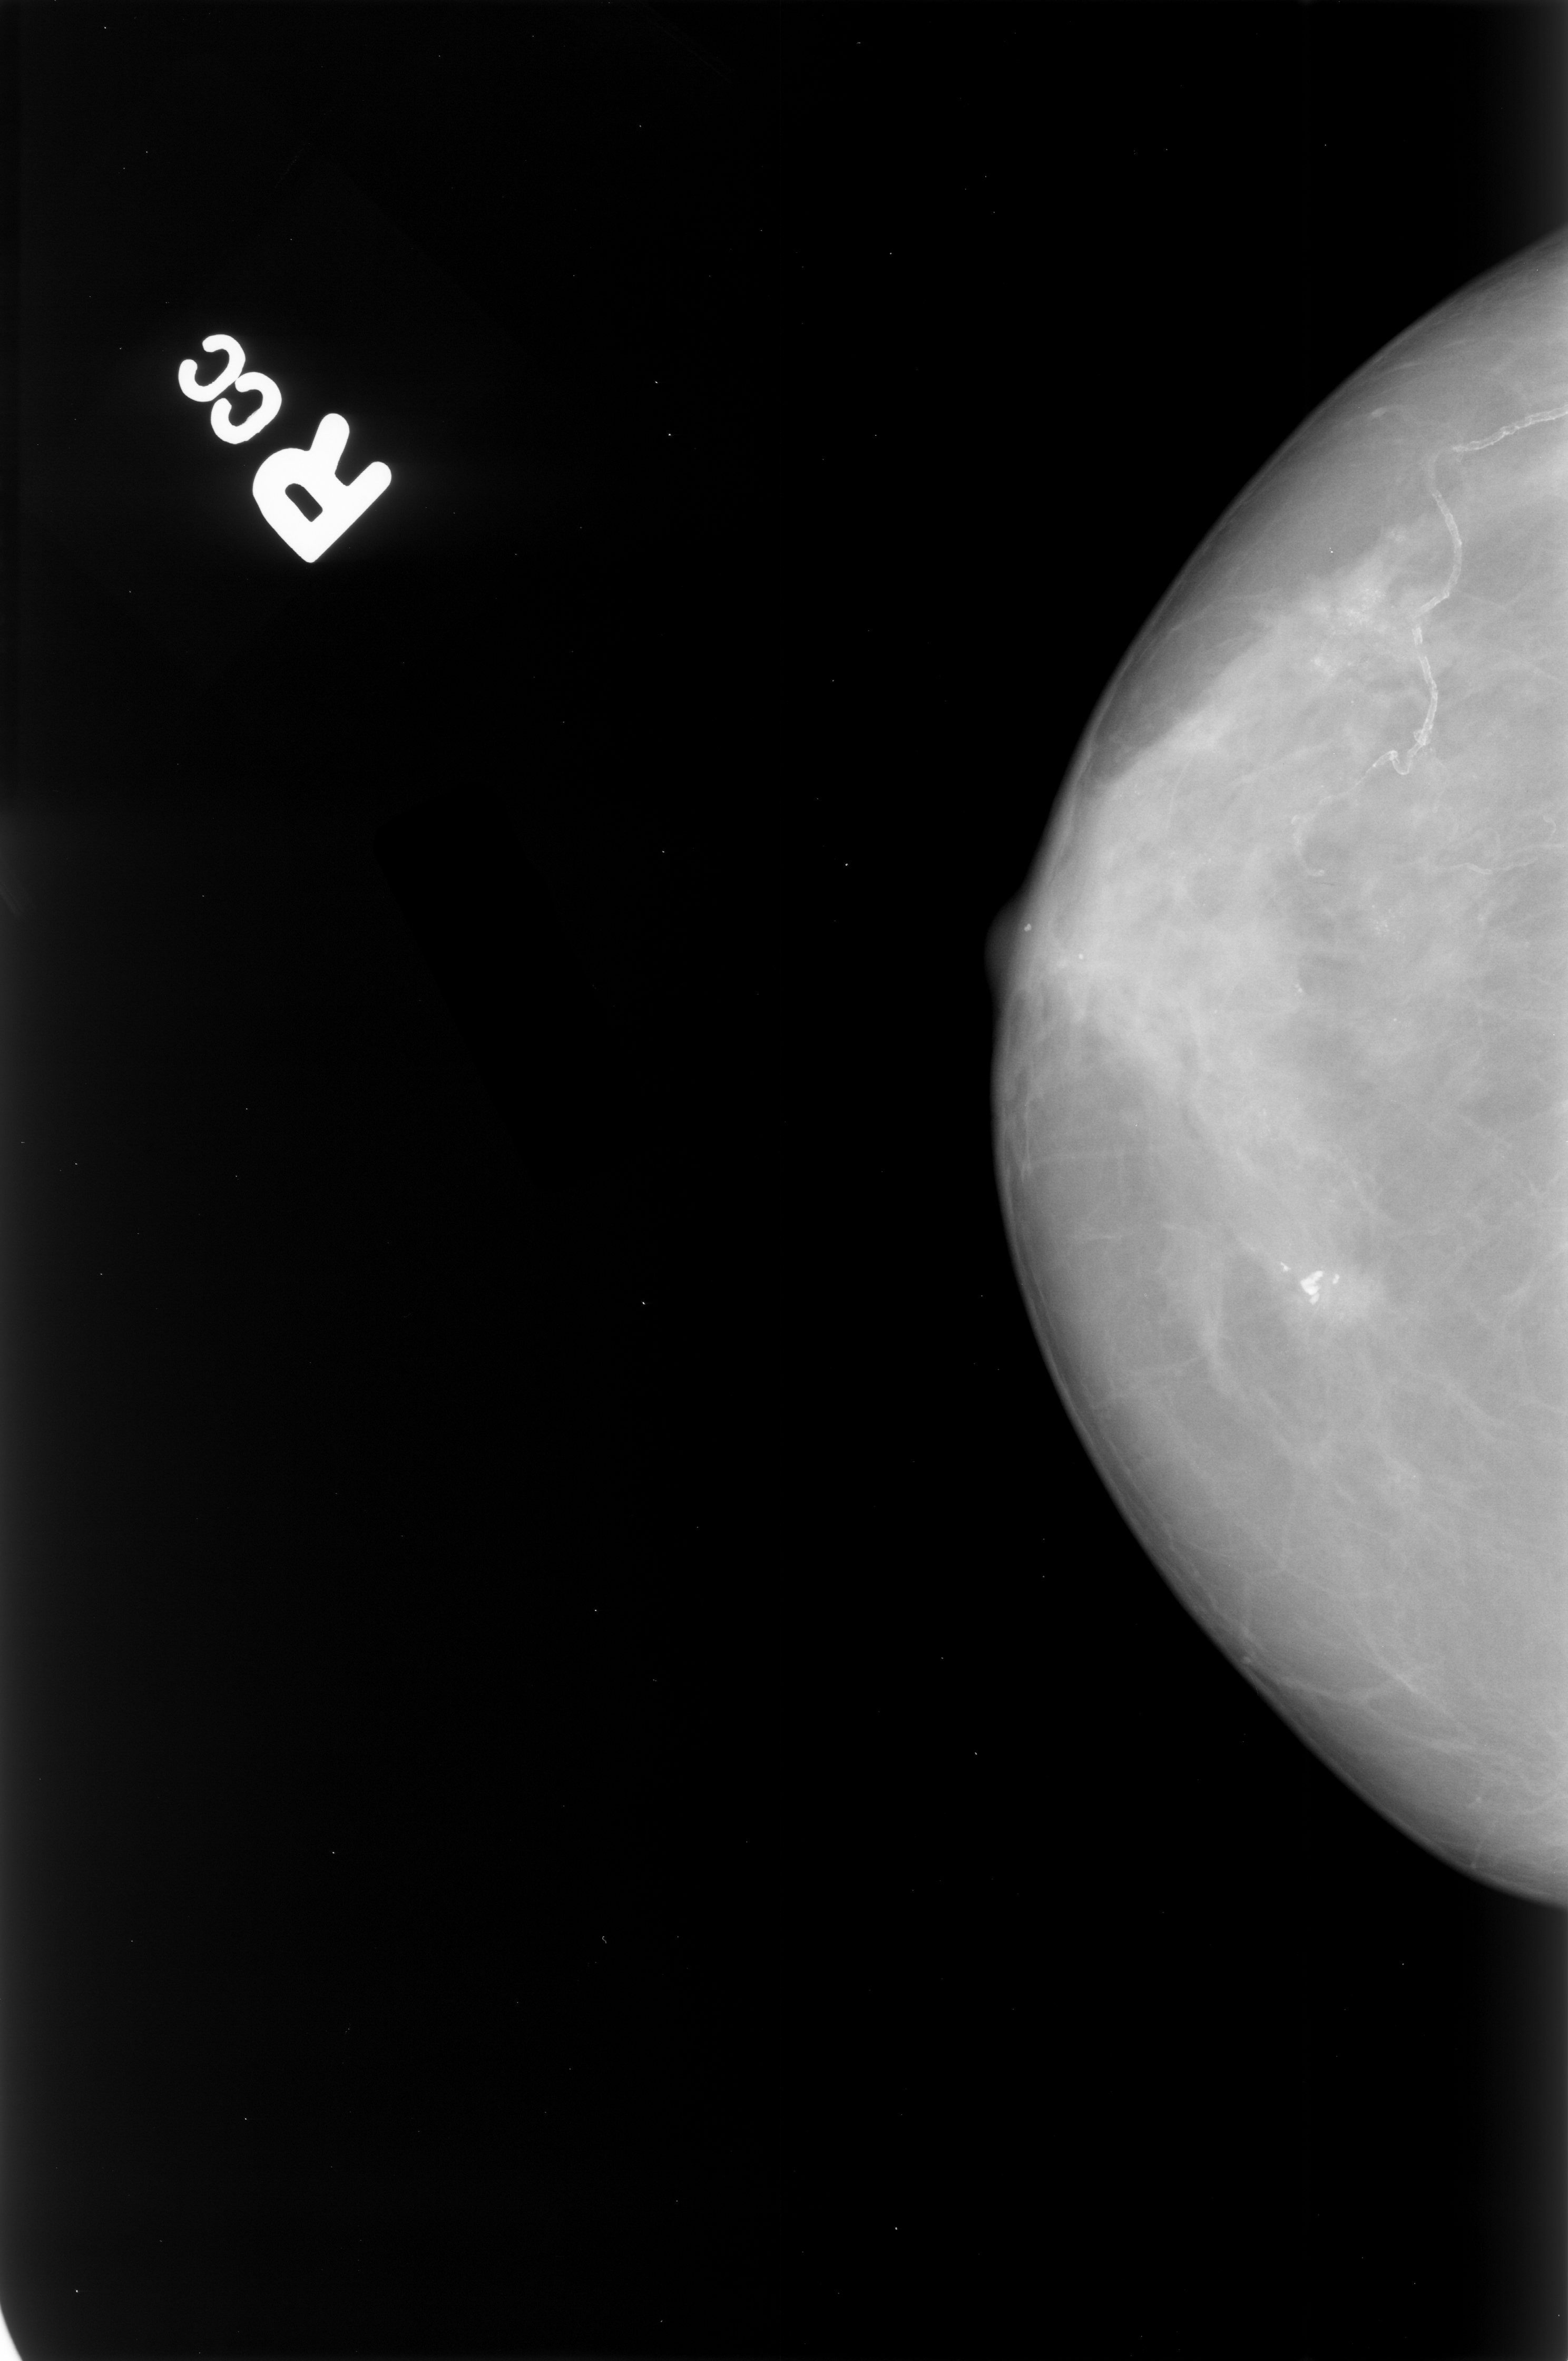
Mammogram (digitized film). Right breast. Craniocaudal (CC) view. BI-RADS breast density category 3 (scale 1–4). 1568 × 2361 image matrix.
Expert-marked regions of interest on this image (one box per marked abnormality):
- calcifications, morphology punctate / pleomorphic, distribution clustered; BI-RADS assessment category 4; pathology result (as recorded, not read from the image): malignant: bounding box (x1, y1, x2, y2) in pixels: (1243, 531, 1468, 713)